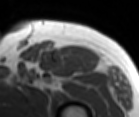
MRI of an extremity soft-tissue mass, one axial slice. Position 80 of 86 along the scan axis. MR volume resampled by the dataset authors to the PET/CT grid (not the native acquisition matrix). 139 × 117 image matrix, field of view 136 × 114 mm. Male patient. Case-level facts recorded for this patient, not image findings: histological type: extraskeletal osteosarcoma; grade: high; site of the primary tumour: thigh.
Structures marked on this image (expert contour drawn on MRI and transferred to this co-registered scan by the dataset authors):
- gross tumour volume (mass): bounding box <63,46,103,67> (left, top, right, bottom; pixels)